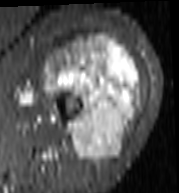
MRI of an extremity soft-tissue mass, one axial slice; slice 64 of 103 in the series (ordered by position); STIR; MR volume resampled by the dataset authors to the PET/CT grid (not the native acquisition matrix); 3.27 mm slice thickness; 179 × 193 image matrix, field of view 175 × 188 mm. Female patient. From the clinical record (not read from this slice): histological type: undifferentiated – high grade; grade: high; site of the primary tumour: left thigh.
Outlined on this slice (expert contour drawn on MRI and transferred to this co-registered scan by the dataset authors):
- gross tumour volume including surrounding oedema: bounding box (x1, y1, x2, y2) in pixels: (43, 35, 142, 164)
- gross tumour volume (mass): (43, 35, 142, 164)